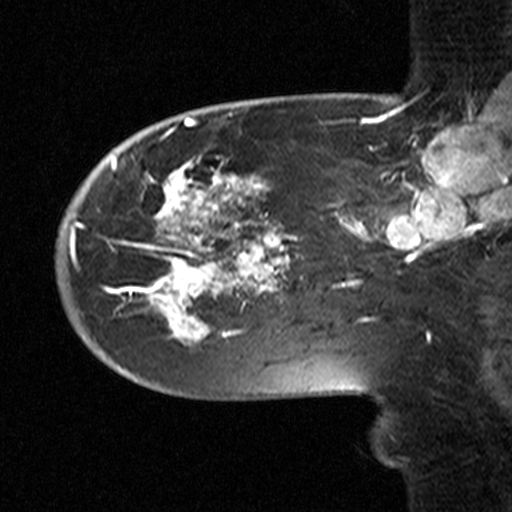
Breast MRI (dynamic contrast-enhanced), one sagittal slice. Dynamic contrast-enhanced study with each time point stored as its own series, time point 2 of 3 at this slice position (early post-contrast, ordered by acquisition time). 1.5 T. TE 4.5 ms, TR 11 ms. 3.27 mm slice thickness. 512 × 512 image matrix, field of view 200 × 200 mm. Patient: female, 53 years. Case-level facts recorded for this patient, not image findings: setting: breast cancer imaged before/during neoadjuvant chemotherapy; receptor status: HR-positive, HER2-negative.
Structures marked on this image (semi-automatically segmented with operator editing):
- analysis volume of interest (the breast-tissue region the enhancement analysis was run in; not a lesion): box from (x=58, y=154) to (x=311, y=367) px
- tumour enhancement mask (voxels above the 90 % enhancement threshold inside the analysis volume of interest): (x=71, y=157)–(x=296, y=341)